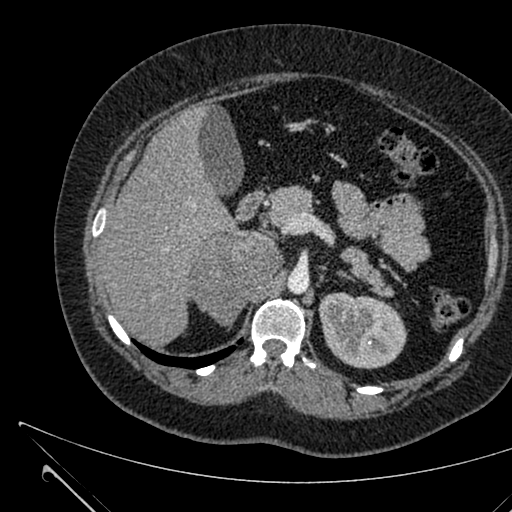
Contrast-enhanced abdominal CT, one axial slice. Position 417 of 731 along the scan axis. Intravenous contrast given. Soft-tissue window (W 400 / L 40 HU). 1 mm slice thickness. 512 × 512 image matrix, field of view 376 × 376 mm. Female patient, age 36 years. Case-level facts recorded for this patient, not image findings: diagnosis: adrenocortical carcinoma; tumour side: right adrenal; tumour size at pathology: 10 cm; Ki-67 index: 20 %.
Outlined on this slice (semi-automatically segmented with operator editing):
- mass: box from (x=191, y=231) to (x=279, y=325) px